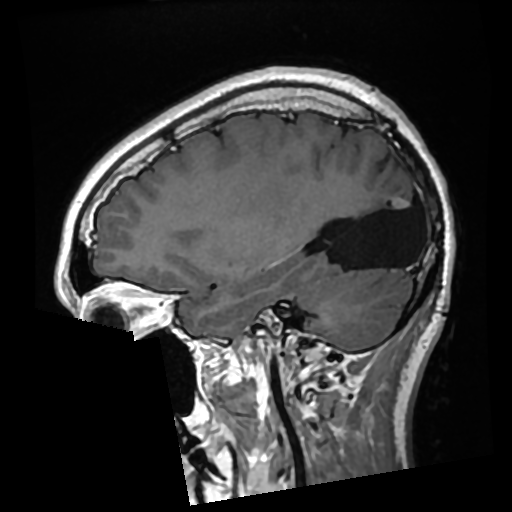
Brain MRI from a brain-tumour surgery series, one sagittal slice. T1-weighted post-contrast. 0.7 mm slice thickness. 512 × 512 image matrix, field of view 250 × 250 mm. Case-level facts recorded for this patient, not image findings: histopathology: Glioma with ependymal features; WHO grade: 2; tumour location: Left Parietal.
Annotated regions visible in this slice (manually delineated by an expert):
- previous resection cavity: box from (x=325, y=182) to (x=419, y=270) px
- tumour: (x=393, y=197)–(x=409, y=209)